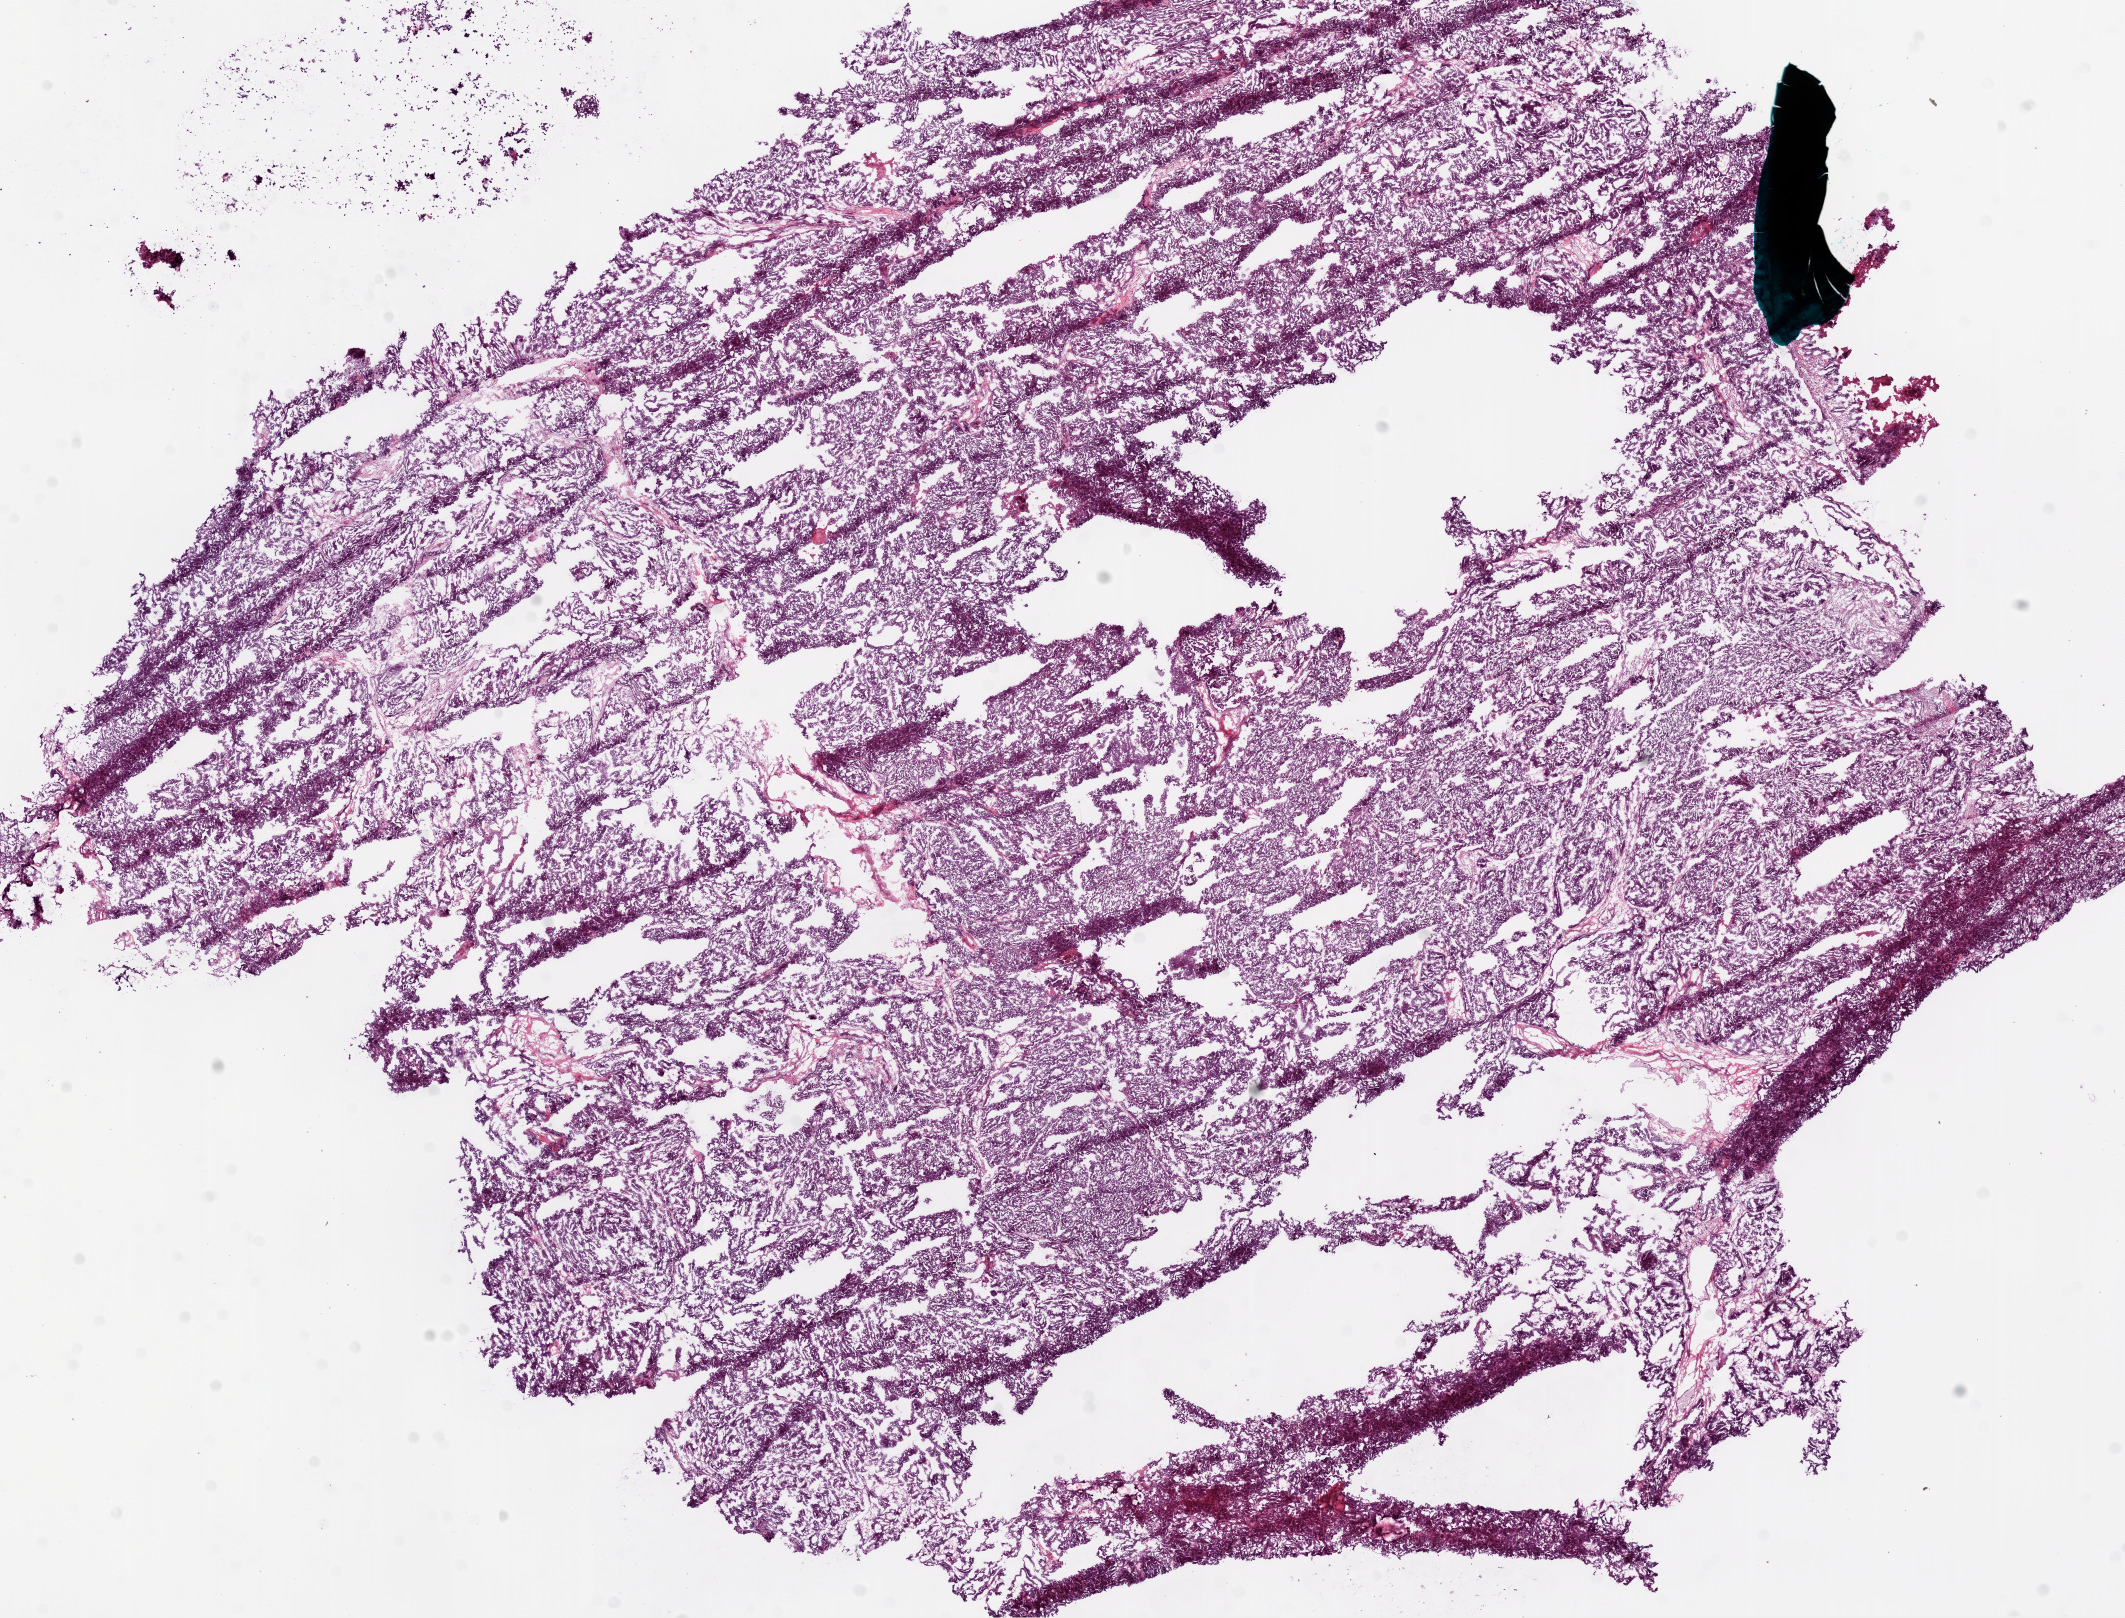
H&E whole-slide image — low-resolution overview of the scanned area, about 17.1 x 13.0 mm, frozen section, primary tumour sample from the ovary. Female, age 68 years at initial diagnosis. Histologic grade: G3 (poorly differentiated). Slide review estimates, as recorded: tumour cells 95%, tumour nuclei 95%, normal cells 0%, stromal cells 5%, necrosis 0%.
- laterality: bilateral
- FIGO stage: IIIC
- diagnosis: Serous cystadenocarcinoma, NOS